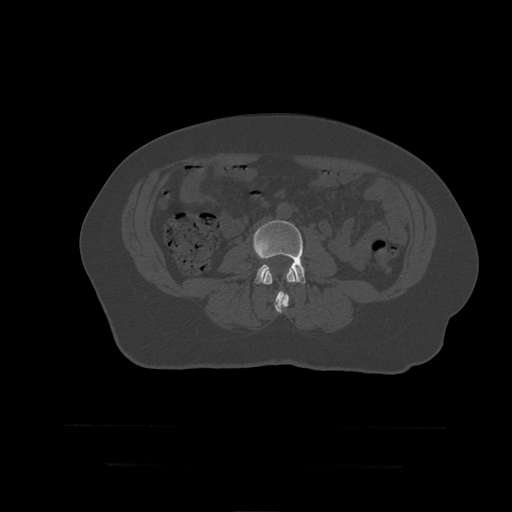
CT including the spine, one axial slice. Slice 108 of 399 in the series (ordered by position). Reconstruction kernel STANDARD. Bone window (W 1800 / L 400 HU). 512 × 512 image matrix, field of view 450 × 450 mm. Patient age 41 years. From the clinical record (not read from this slice): primary cancer: breast.
Annotated regions visible in this slice (semi-automatic segmentation, software-assisted and operator-edited):
- L3 vertebra: bounding box <263,268,296,314> (left, top, right, bottom; pixels)
- L4 vertebra: <253,220,306,285>